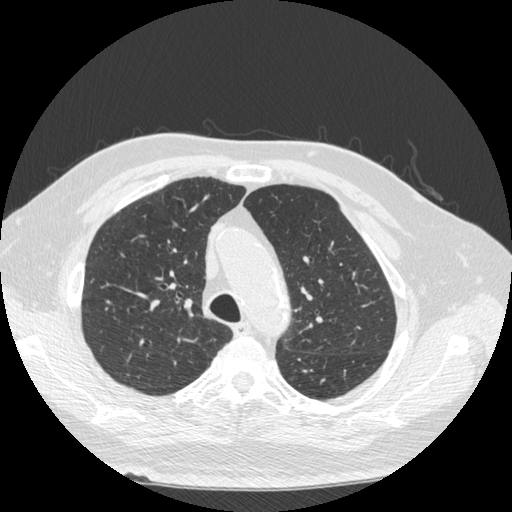
Axial slice from a low-dose chest CT screening exam; second screening round (one year after baseline); lung window (W 1500 / L -600 HU); 1.25 mm slice thickness; standard (soft-tissue) reconstruction kernel (STANDARD); 120 kVp; slice 157 of 221 in the series. Male, age 72 years at enrolment. Former smoker at enrolment.
- Lesion marked by an expert reader, box from (x=86, y=292) to (x=126, y=325) px.
- No non-calcified nodule or mass ≥4 mm was recorded by the screening reader at this exam.
- Official screen result: negative screen, minor abnormalities not suspicious for lung cancer.
- Lung cancer was diagnosed 449 days after this screen (after the third annual screen): squamous cell carcinoma, NOS, right upper lobe, poorly differentiated (G3), stage IIIA (AJCC 6th edition), 19 mm at pathology.